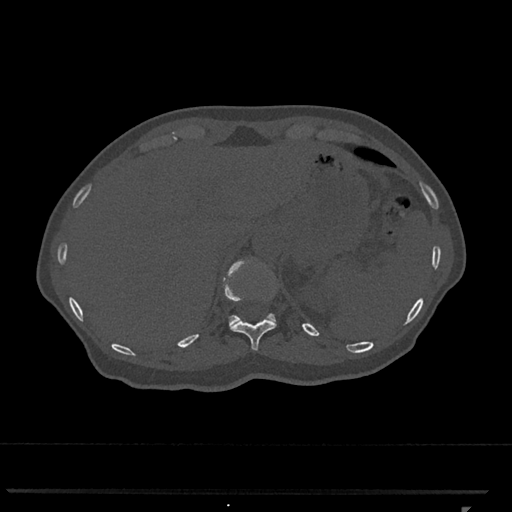
CT including the spine, one axial slice. Position 500 of 793 along the scan axis. 120 kVp. Bone window (W 1800 / L 400 HU). 0.5 mm slice thickness. 512 × 512 image matrix. Female patient, age 62 years. Case-level facts recorded for this patient, not image findings: primary cancer: renal.
Structures marked on this image (semi-automatic segmentation, software-assisted and operator-edited):
- T11 vertebra: bounding box <229,260,277,351> (left, top, right, bottom; pixels)
- T12 vertebra: <223,259,276,325>